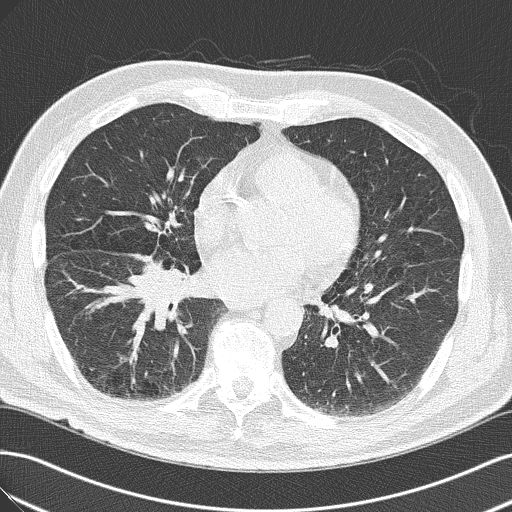
Low-dose screening chest CT, axial slice. Baseline annual screen. Lung window (W 1500 / L -600 HU). 2 mm slice thickness. 120 kVp. 512 × 512 image matrix, field of view 360 × 360 mm. Male, age 65 years at enrolment. Current smoker at enrolment.
• Expert reader's lesion annotation, bounding box (x1, y1, x2, y2) in pixels: (103, 249, 205, 339).
• Screening reader's record for this exam (one nodule recorded; not confirmed to be the boxed lesion): non-calcified nodule or mass ≥4 mm, right upper lobe, 18 × 13 mm, spiculated (stellate) margins, soft tissue attenuation.
• Later outcome: lung cancer diagnosed 14 days after this screen — adenocarcinoma, NOS, right lower lobe, poorly differentiated (G3), stage IIIA (AJCC 6th edition), 40 mm at pathology.